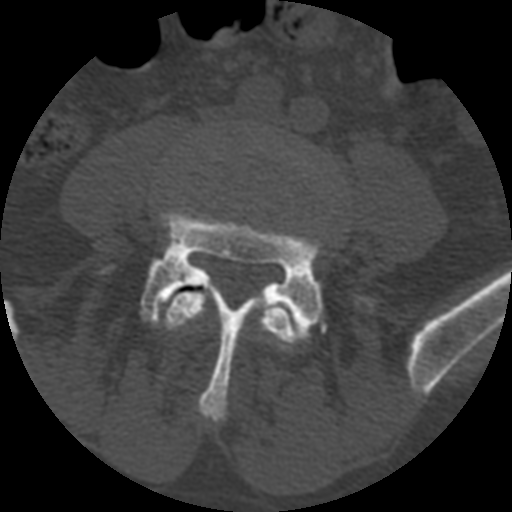
CT including the spine, one axial slice. Position 265 of 399 along the scan axis. Reconstruction kernel STANDARD. Bone window (W 1800 / L 400 HU). 1.25 mm slice thickness. 512 × 512 image matrix, field of view 160 × 160 mm. Patient age 71 years. From the clinical record (not read from this slice): primary cancer: prostate.
Structures marked on this image (semi-automatic segmentation, software-assisted and operator-edited):
- L4 vertebra: bounding box <164,291,299,349> (left, top, right, bottom; pixels)
- L5 vertebra: <140,208,377,422>